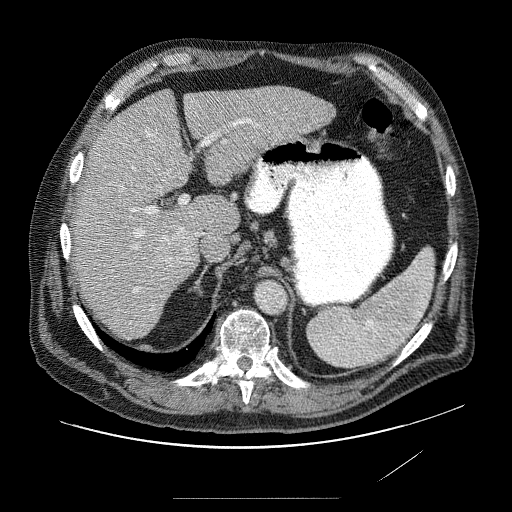
Contrast-enhanced abdominal CT (liver protocol), one axial slice. Slice 52 of 89 in the series (ordered by position). Reconstruction kernel STANDARD. 120 kVp. Soft-tissue window (W 400 / L 40 HU). 512 × 512 image matrix, field of view 420 × 420 mm. Case-level facts recorded for this patient, not image findings: diagnosis: hepatocellular carcinoma (patient treated with transarterial chemoembolisation; whether this scan precedes or follows treatment is not stated here); TNM stage (as recorded): Stage-IVA; Child-Pugh class: A; tumour differentiation: moderately differentiated; tumour nodularity: multinodular.
Annotated regions visible in this slice (semi-automatic segmentation, software-assisted and operator-edited):
- abdominal aorta: bounding box [x1, y1, x2, y2] px = [255, 282, 285, 313]
- liver parenchyma outside the tumour (the mass and vessels are separate outlines, so this box may not span the whole liver): [72, 86, 338, 328]
- mass: [151, 140, 195, 184]
- liver vessels: [126, 116, 292, 297]